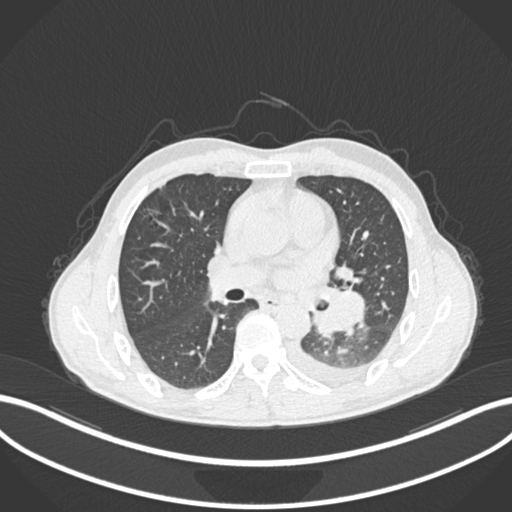
Chest CT, one axial slice; slice 132 of 222 in the series (ordered by position); reconstruction kernel B30f; lung window (W 1500 / L -600 HU); 1 mm slice thickness; 512 × 512 image matrix, field of view 400 × 400 mm. Male patient, age 47 years. From the clinical record (not read from this slice): clinical TNM (as recorded): T3 N1 M1c; histopathological grade: G3.
Annotated regions visible in this slice (rectangle marked by the reading radiologist):
- lung tumour (recorded histology: small cell carcinoma): bounding box [x1, y1, x2, y2] px = [309, 283, 369, 342]